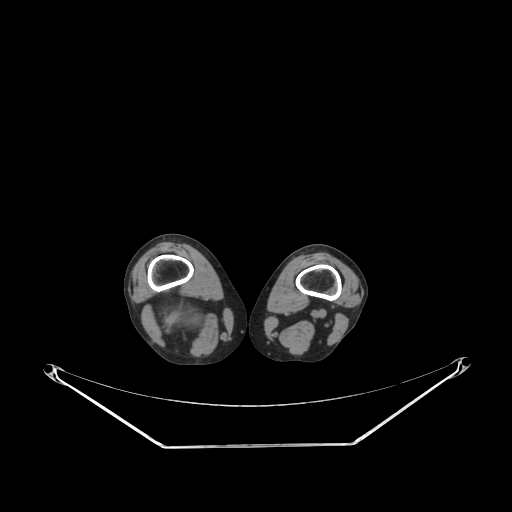
CT of an extremity soft-tissue mass (from a PET/CT study), one axial slice; position 186 of 267 along the scan axis; 140 kVp; soft-tissue window (W 400 / L 40 HU); 3.75 mm slice thickness; 512 × 512 image matrix. Female patient. Case-level facts recorded for this patient, not image findings: histological type: liposarcoma; site of the primary tumour: right thigh.
Structures marked on this image (expert contour drawn on MRI and transferred to this co-registered scan by the dataset authors):
- gross tumour volume (mass): bounding box [x1, y1, x2, y2] px = [155, 297, 209, 337]